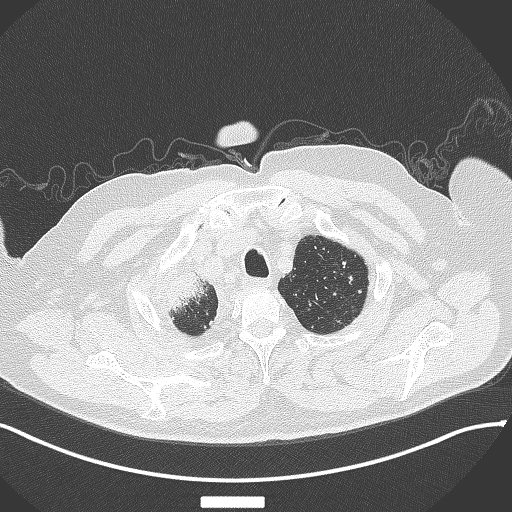
Chest CT, one axial slice. Position 329 of 384 along the scan axis. 120 kVp. Lung window (W 1500 / L -600 HU). 1 mm slice thickness. 512 × 512 image matrix, field of view 400 × 400 mm. Patient: male, 69 years. From the clinical record (not read from this slice): clinical TNM (as recorded): T4 N3 M1.
Annotated regions visible in this slice (rectangle marked by the reading radiologist):
- lung tumour (recorded histology: adenocarcinoma): bounding box (x1, y1, x2, y2) in pixels: (158, 264, 208, 313)